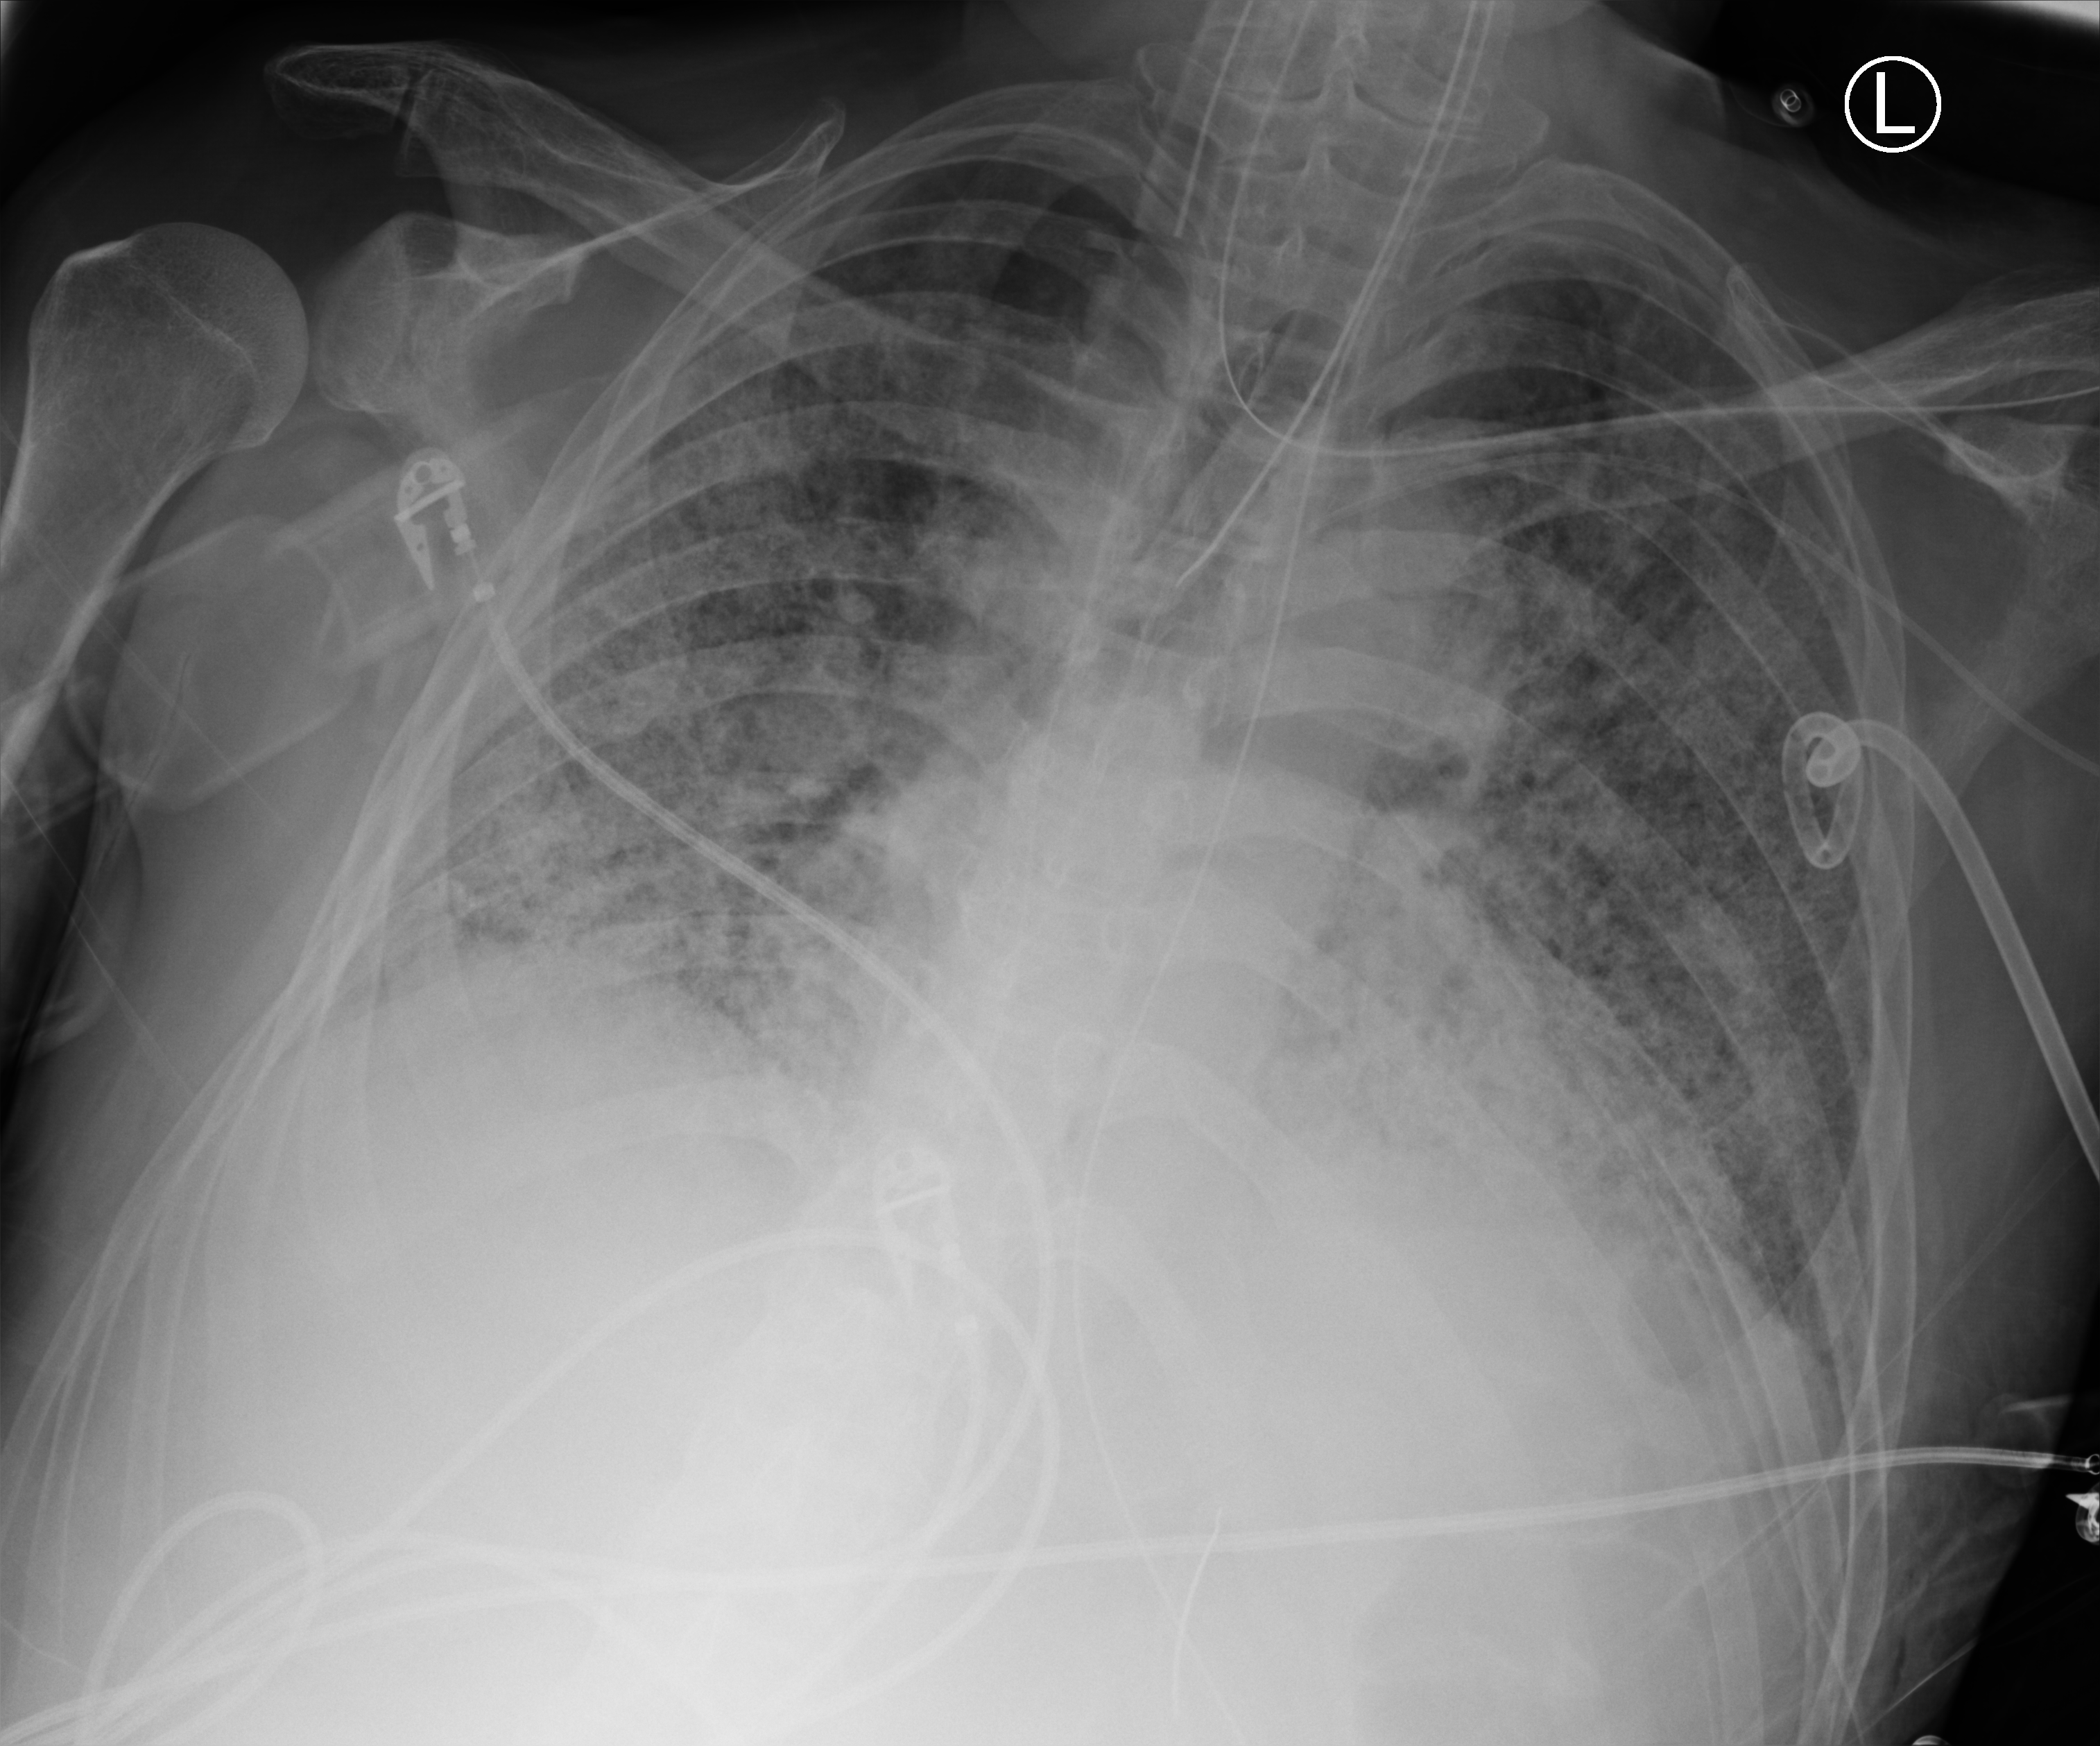
Chest X-ray (portable), anteroposterior (AP) projection. Patient hospitalised with COVID-19; male, aged 60–74 years.
Hospital-stay facts (about this admission, not read from this image; timing relative to this image not recorded): mechanically ventilated during this hospital stay: yes.